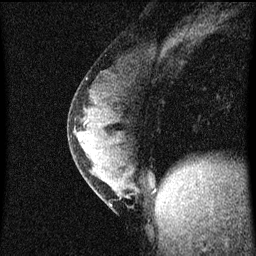
Breast MRI (dynamic contrast-enhanced), one sagittal slice; position 26 of 60 along the scan axis; dynamic contrast-enhanced series, image 2 of 4 at this slice position (ordered by acquisition); 1.5 T; TE 4.2 ms, TR 8 ms; 2 mm slice thickness; 256 × 256 image matrix. Female patient, age 33 years.
Outlined on this slice (semi-automatically segmented with operator editing):
- analysis volume of interest (the breast-tissue region the enhancement analysis was run in; not a lesion): bounding box <69,76,147,211> (left, top, right, bottom; pixels)
- tumour enhancement mask (voxels above the 70 % enhancement threshold inside the analysis volume of interest): <78,138,111,205>